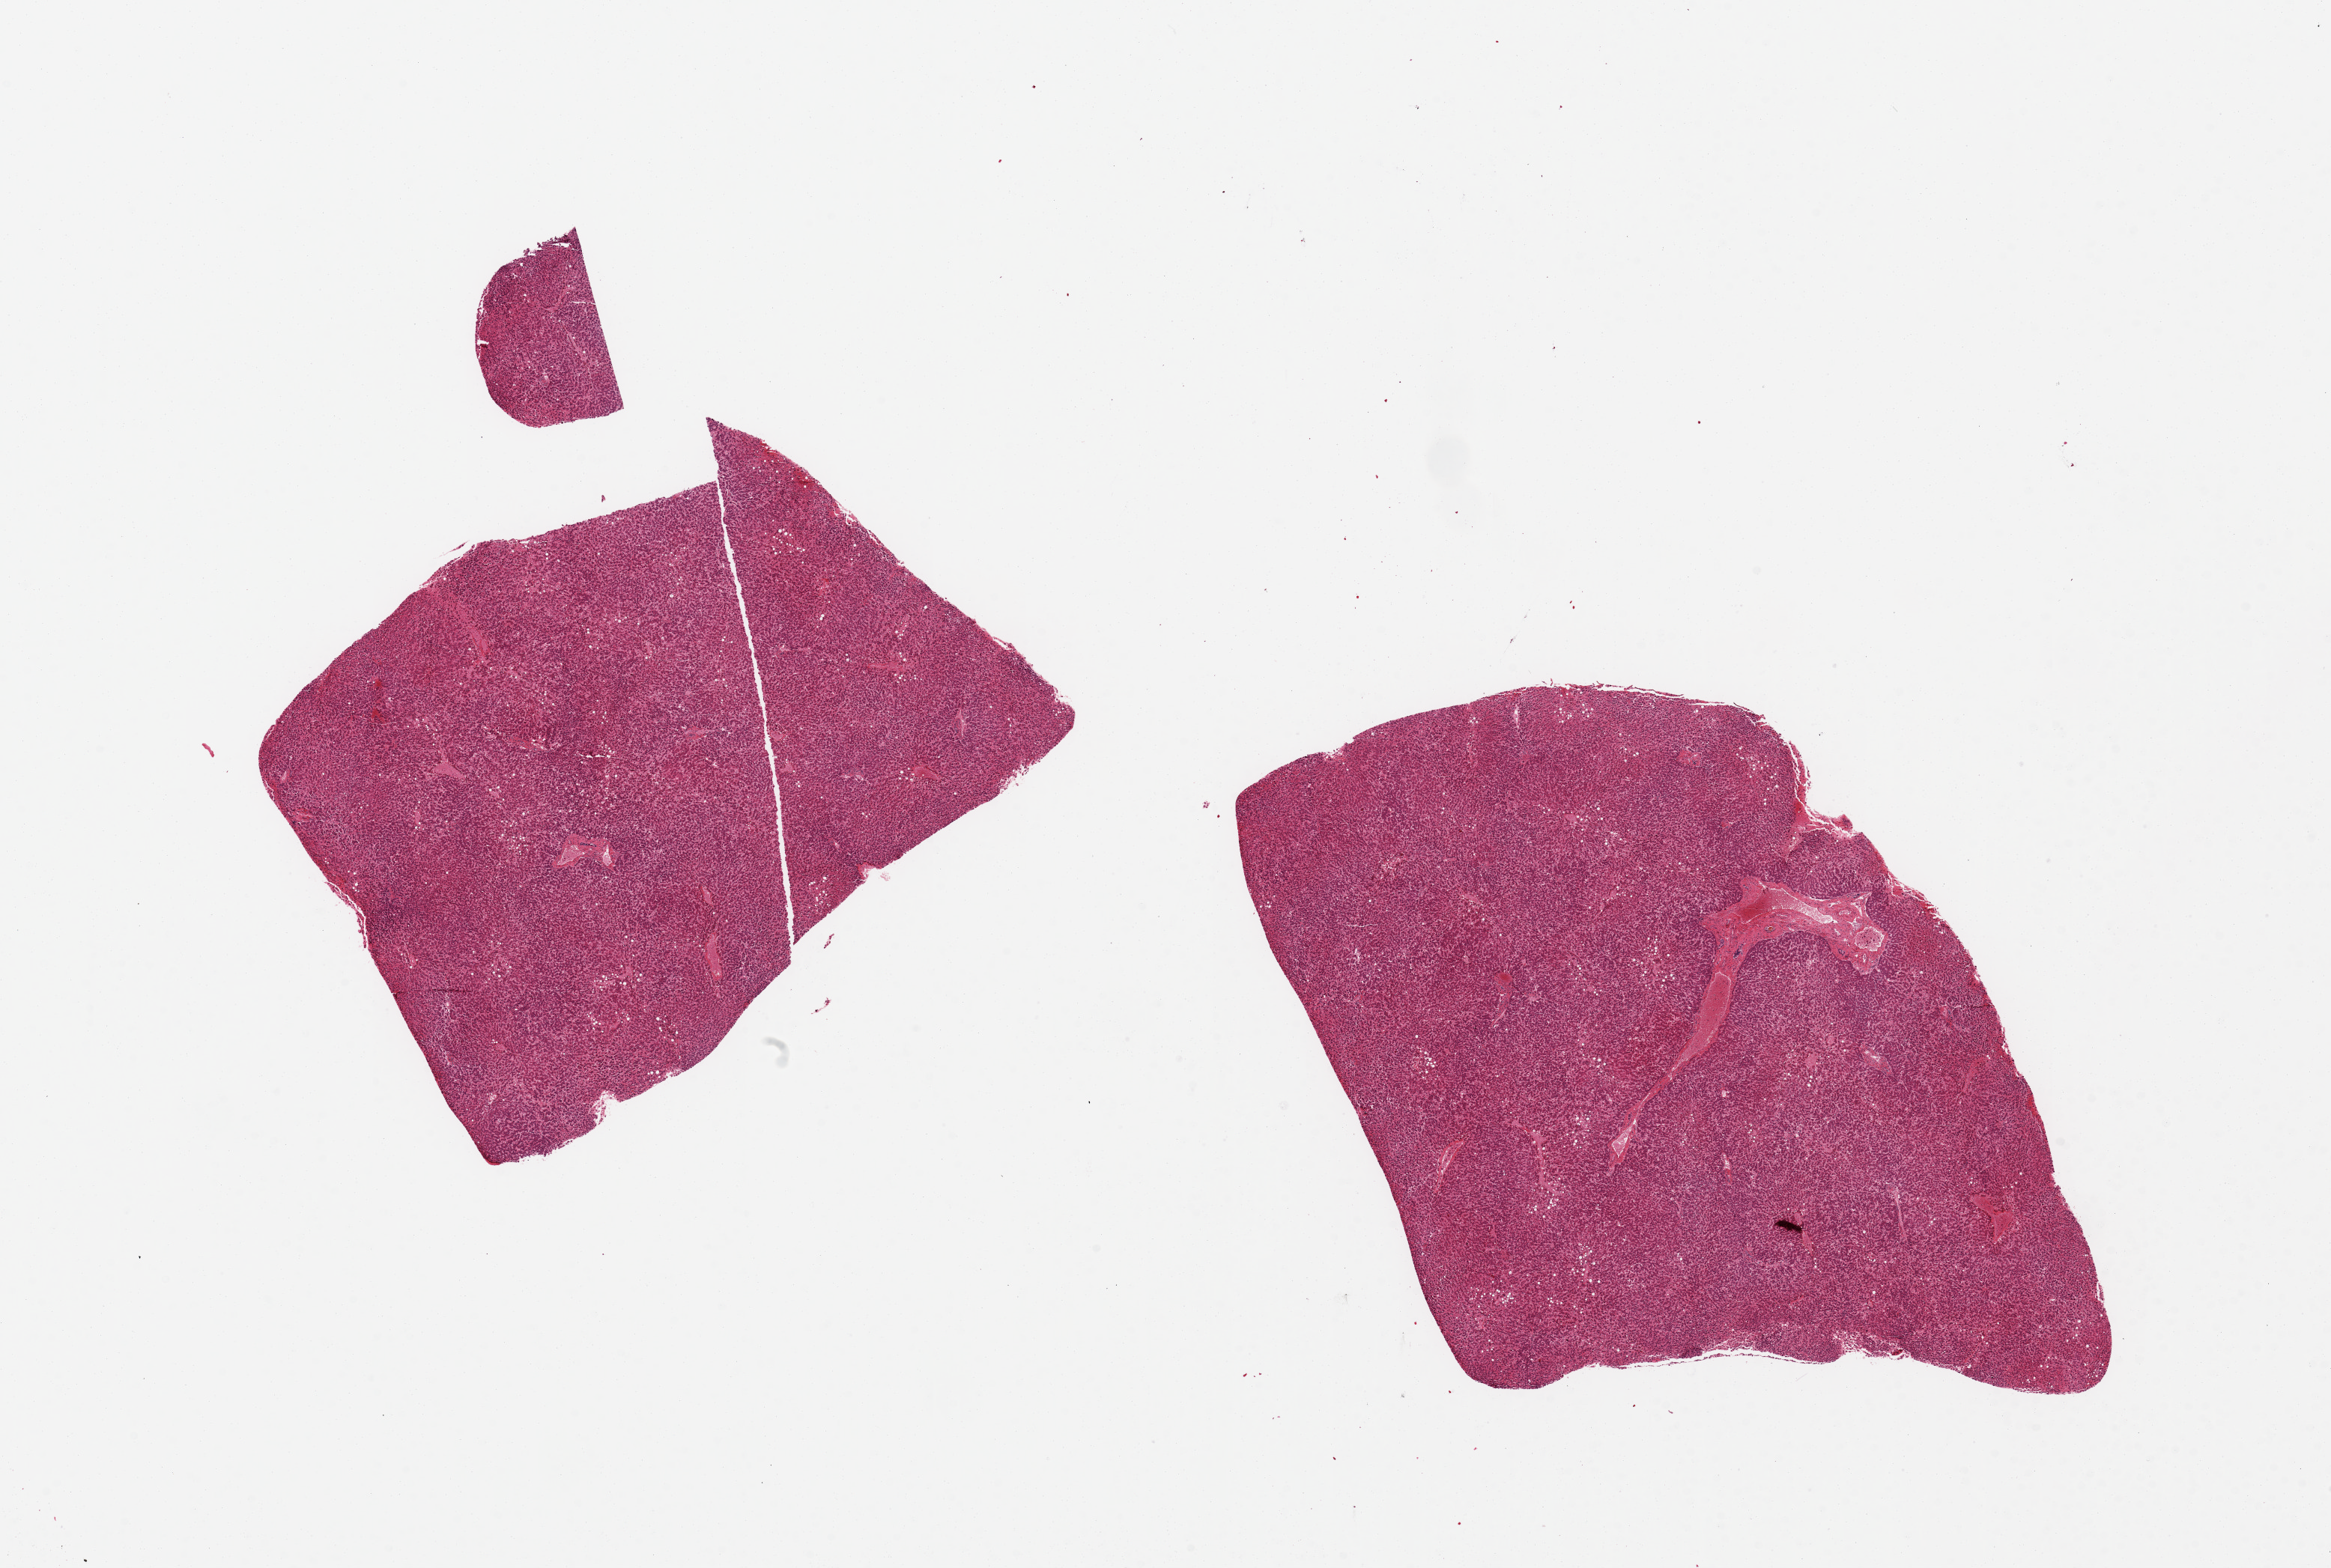
Haematoxylin and eosin whole-slide image, a low-resolution overview of the entire scanned area, about 24.6 x 16.6 mm; PAXgene-fixed, paraffin-embedded tissue; section of liver (target tissue); donor tissue sample. Donor: male.
Review note (as recorded): 2 pieces, 5.5x8 & 6x8mm; mild macrovesicular steatosis.